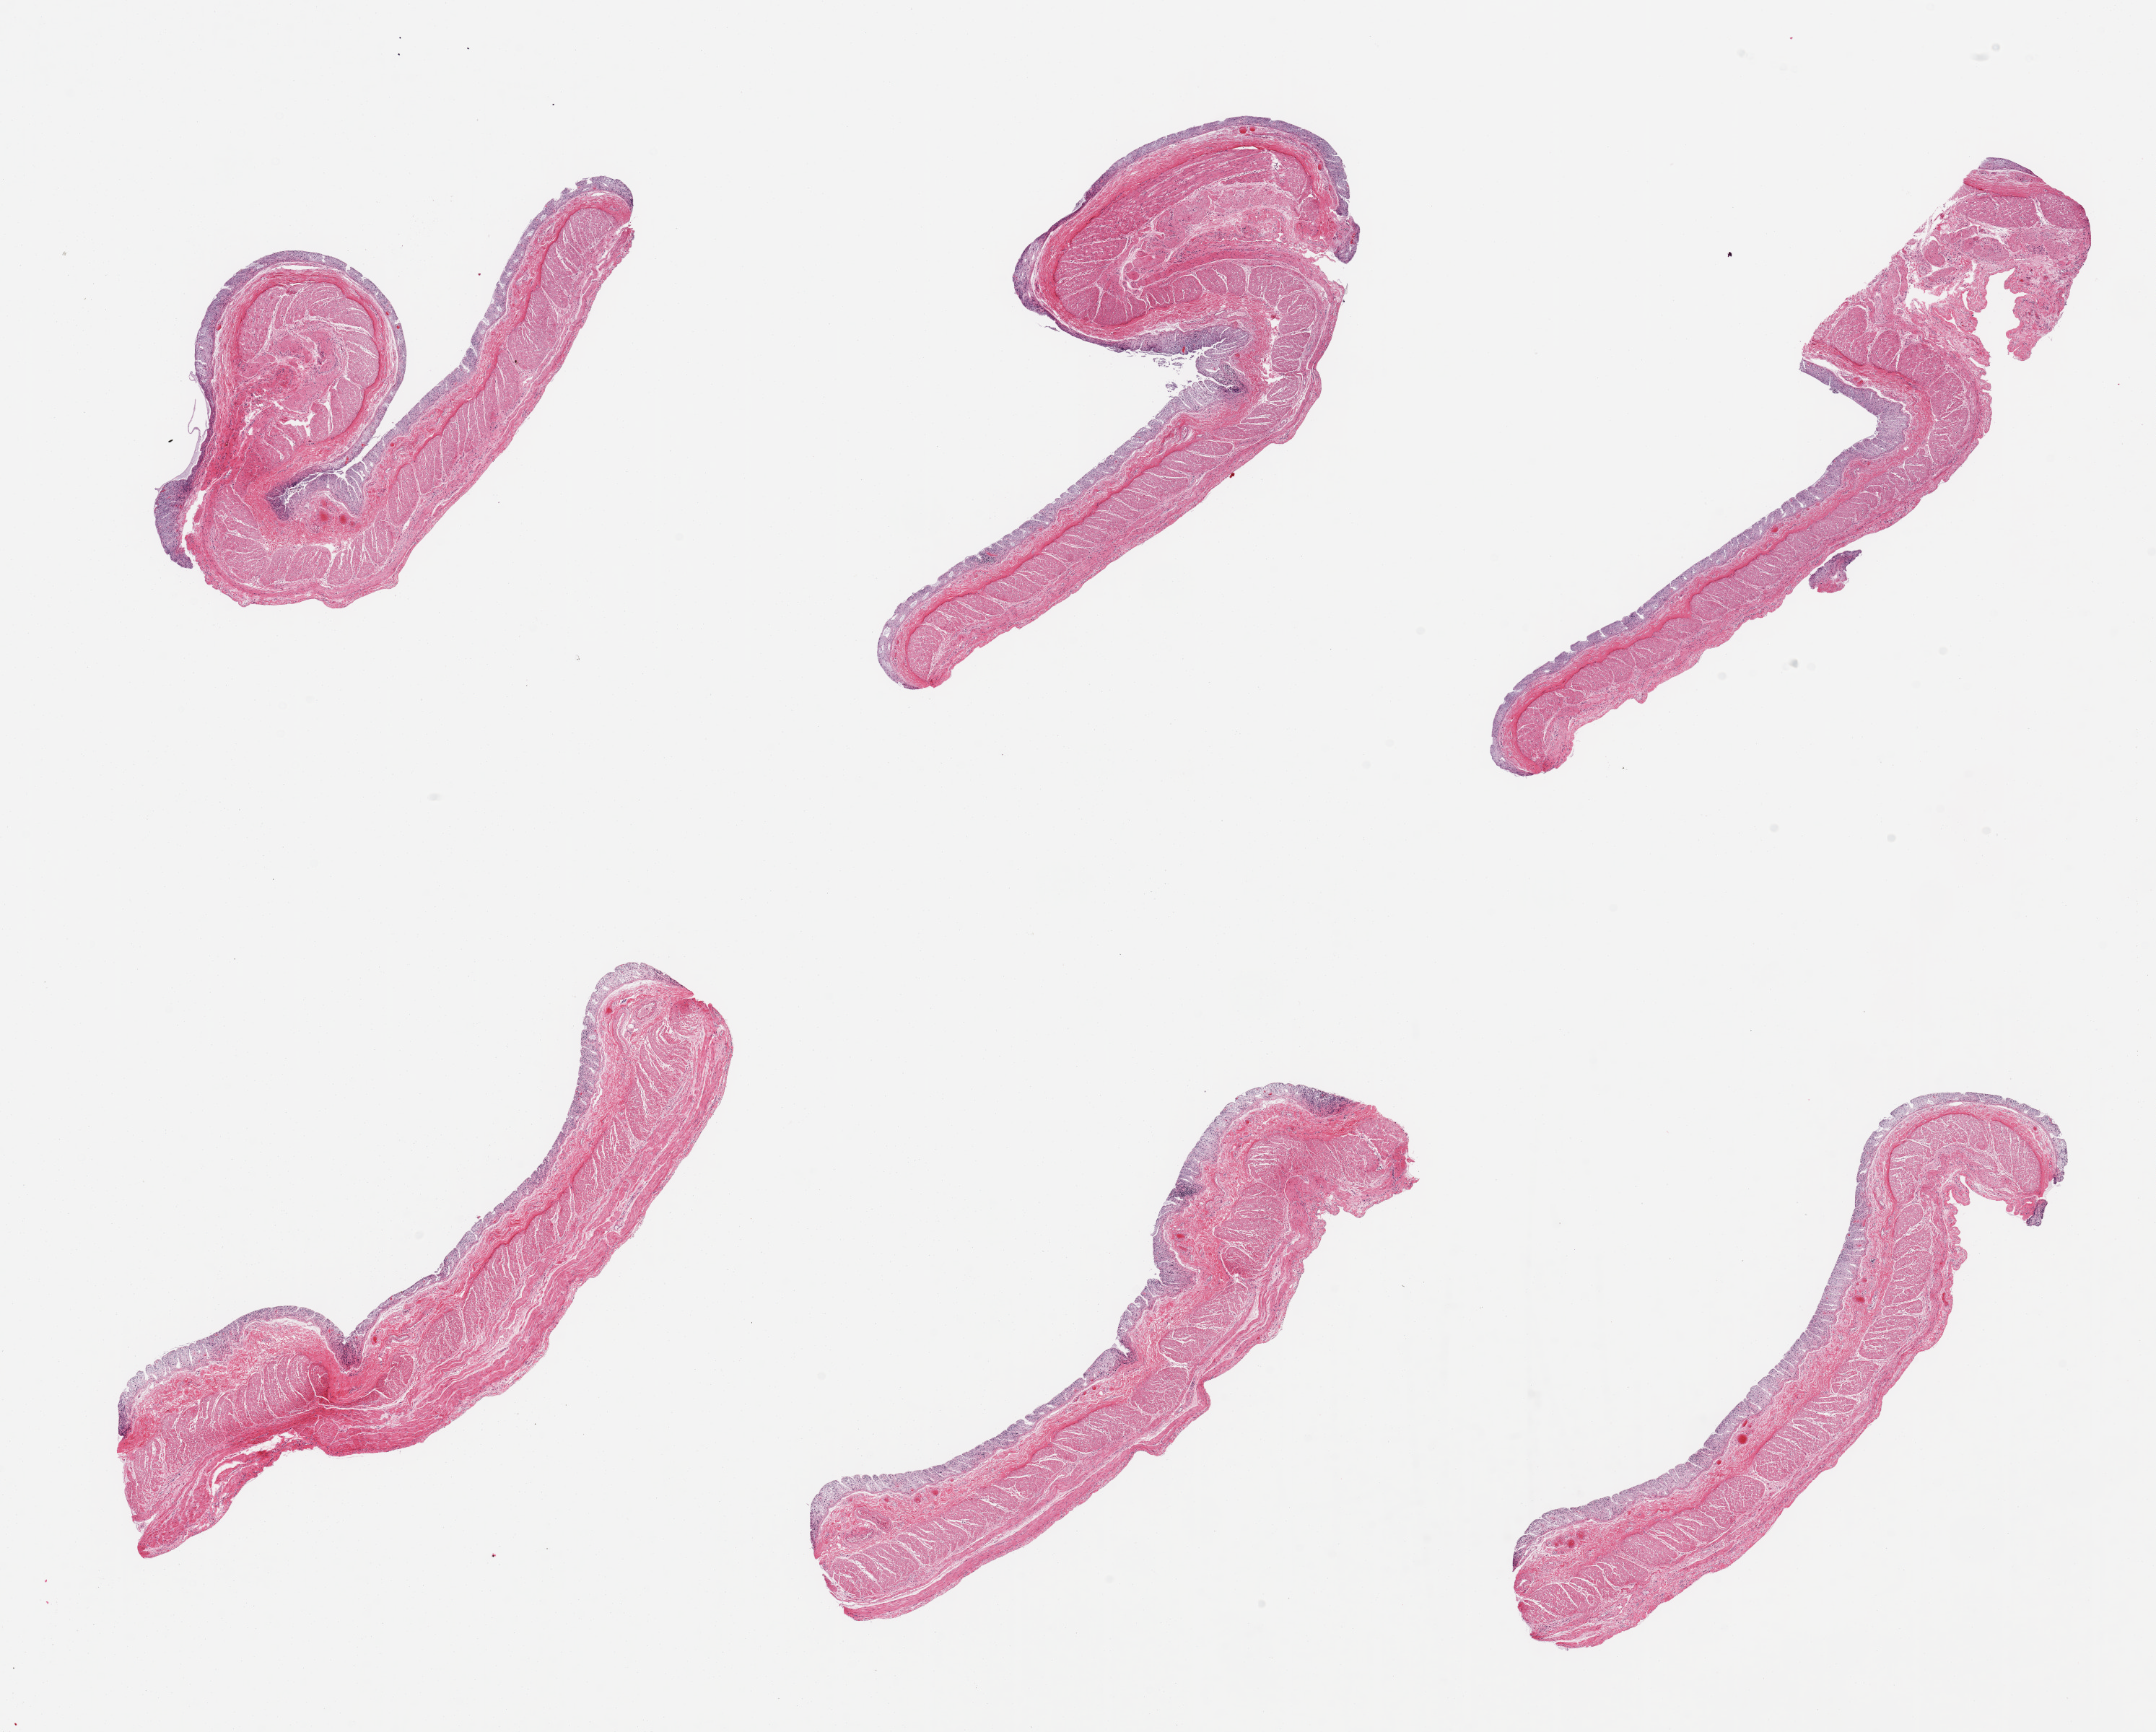
H&E whole-slide image, brightfield, whole scanned area (about 23.6 x 19.0 mm) shown as a low-resolution overview; PAXgene-fixed, paraffin-embedded tissue; target tissue: transverse colon; tissue donor sample.
• review note (as recorded): 6 pieces; mucosa autolyzed, muscularis intact